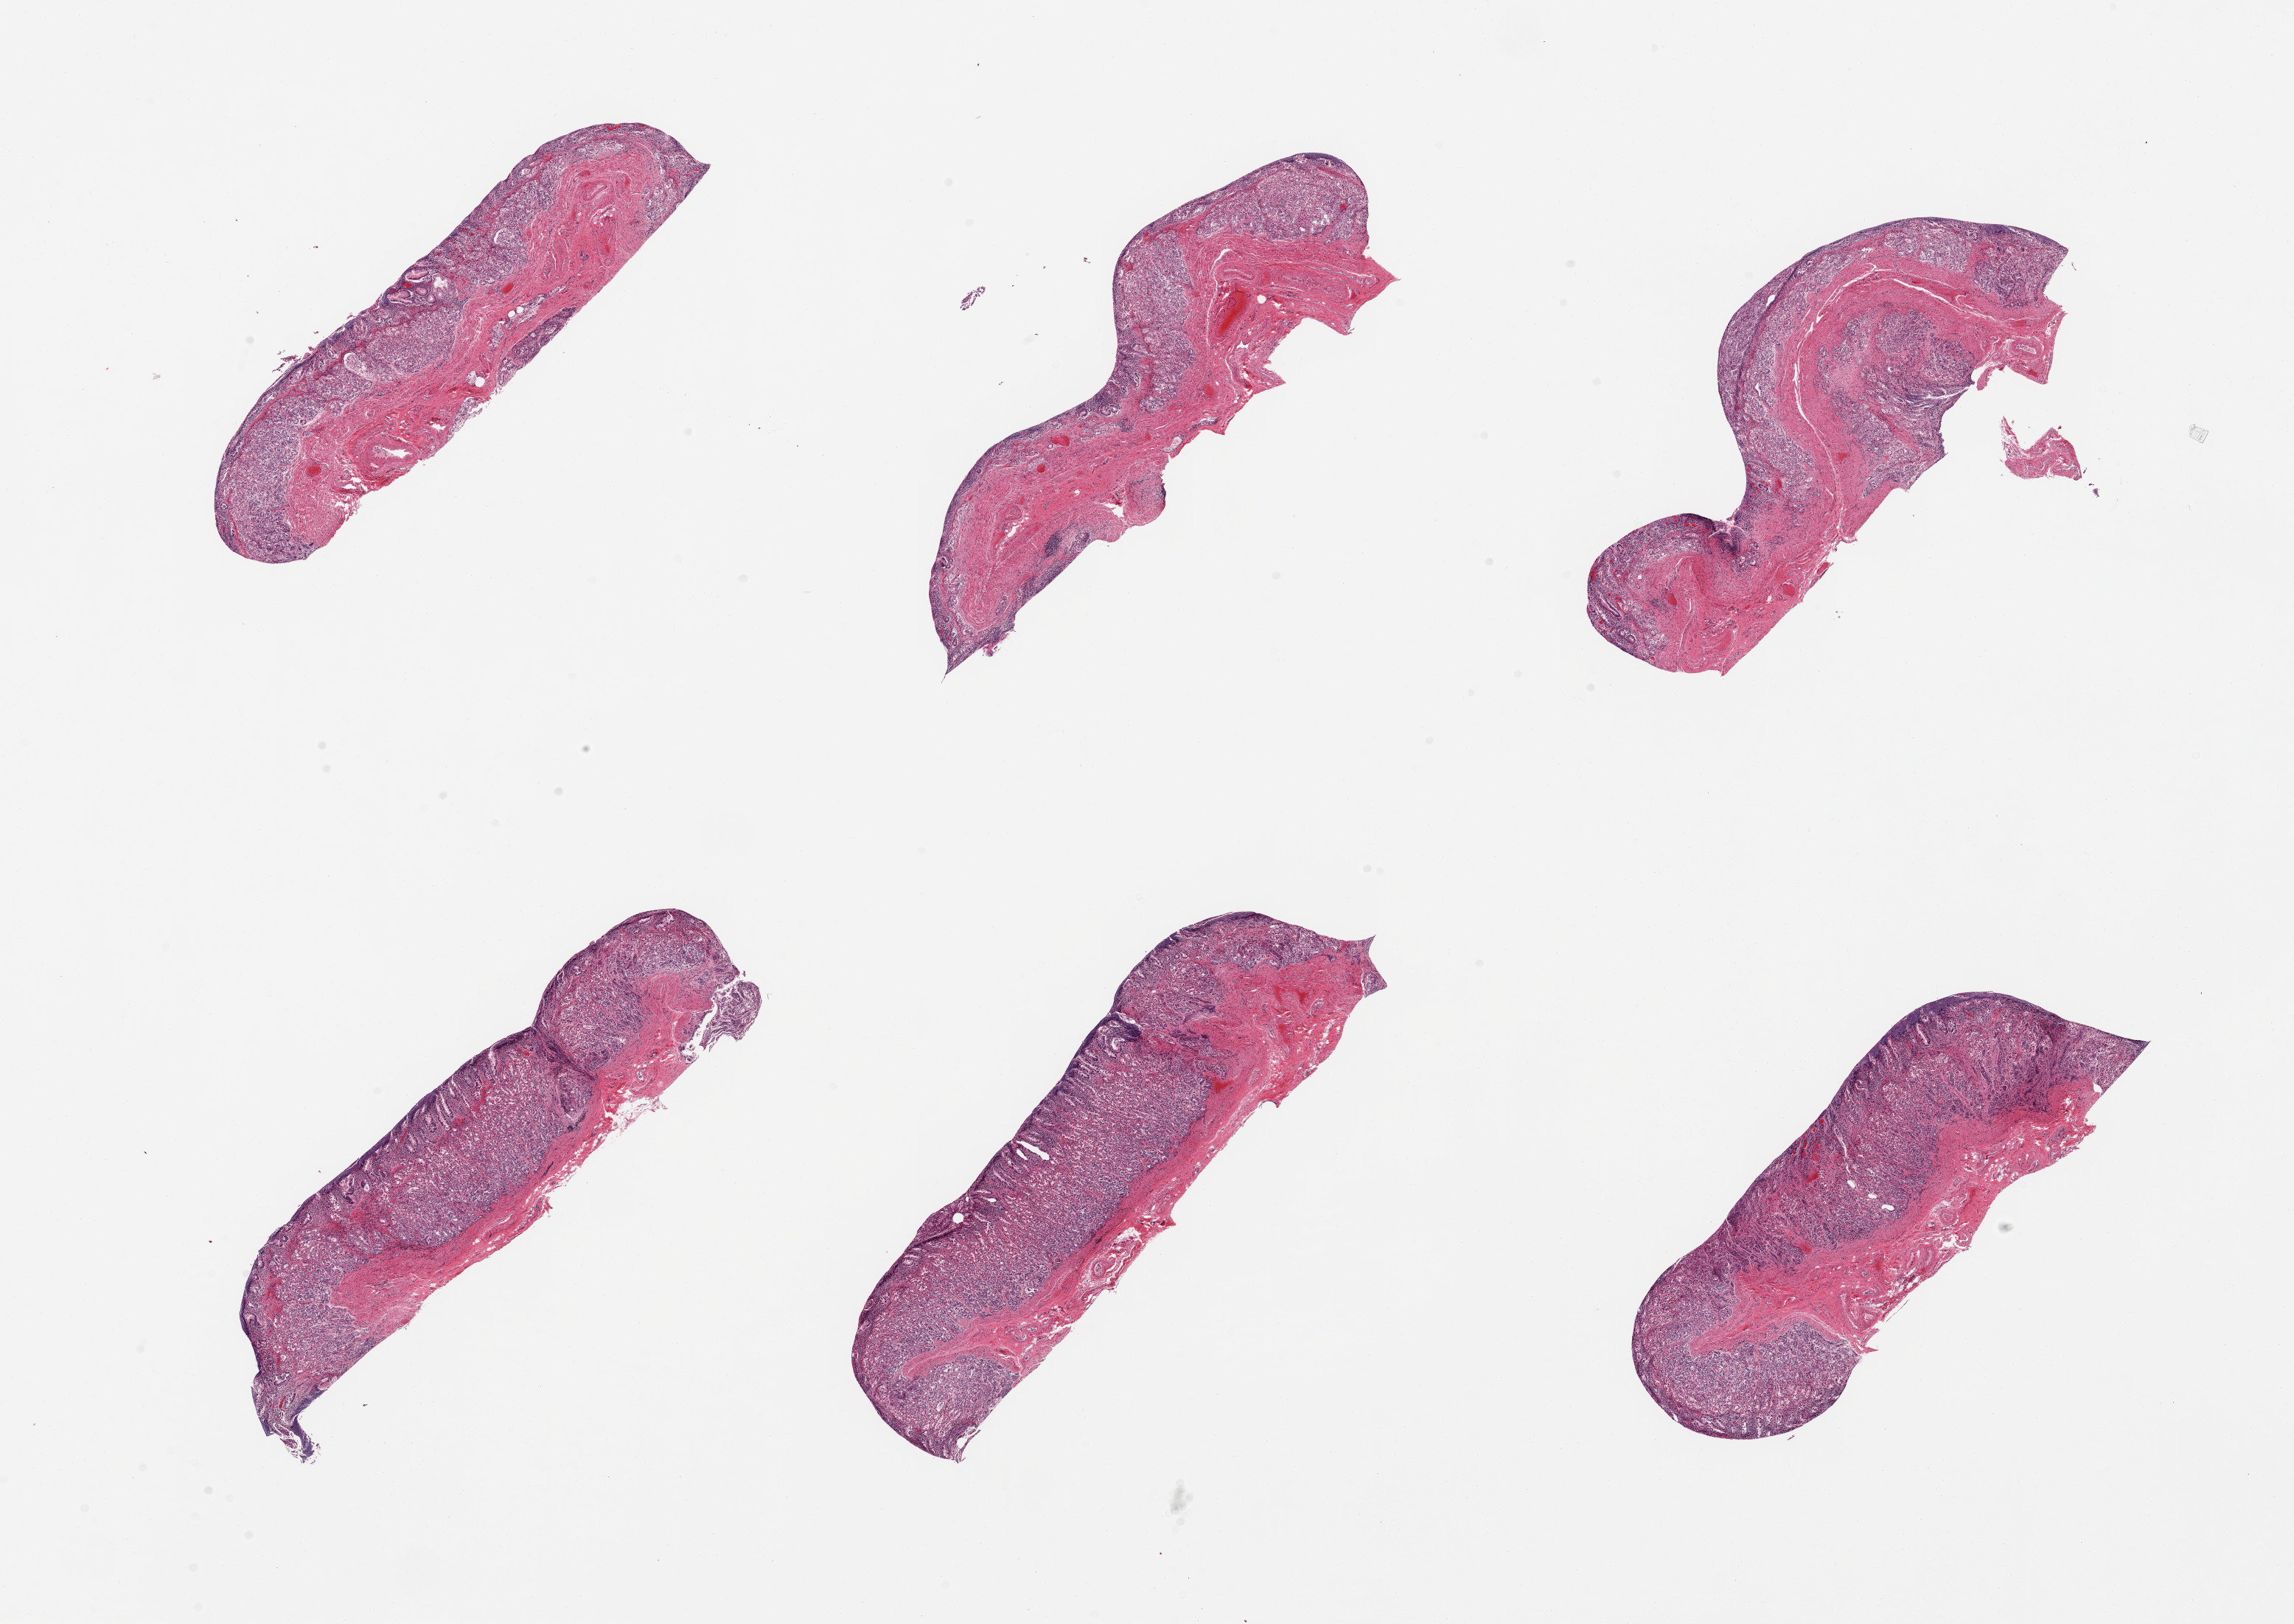
Haematoxylin and eosin whole-slide image, a low-resolution overview of the entire scanned area, about 24.6 x 17.4 mm. PAXgene-fixed, paraffin-embedded tissue. Target tissue: esophageal mucous membrane. Donor tissue sample. Donor sex: male.
Review note (as recorded): 6 pieces; autolyzed gastric fundic mucosa with chronic gastritis; likely represents gastric mucosa in a hiatus hernia rather than glandular metaplasia or sampling error.